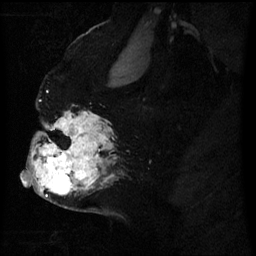
Breast MRI (dynamic contrast-enhanced), one sagittal slice; position 40 of 60 along the scan axis; dynamic contrast-enhanced series, image 2 of 3 at this slice position (ordered by acquisition); 1.5 T; TE 4.2 ms, TR 8 ms; 2.5 mm slice thickness; 256 × 256 image matrix. Female patient, age 50 years.
Annotated regions visible in this slice (semi-automatically segmented with operator editing):
- analysis volume of interest (the breast-tissue region the enhancement analysis was run in; not a lesion): box from (x=24, y=116) to (x=109, y=199) px
- tumour enhancement mask (voxels above the 70 % enhancement threshold inside the analysis volume of interest): (x=24, y=126)–(x=104, y=193)